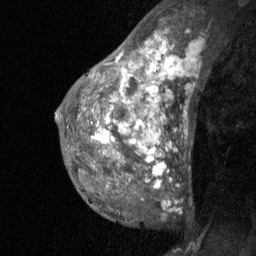
Breast MRI (dynamic contrast-enhanced), one sagittal slice. Slice 40 of 64 in the series (ordered by position). Dynamic contrast-enhanced study with each time point stored as its own series, time point 2 of 3 at this slice position (early post-contrast, ordered by acquisition time). 1.5 T. TE 4.8 ms, TR 27 ms. 2 mm slice thickness. 256 × 256 image matrix, field of view 180 × 180 mm. Patient: female, 36 years. Case-level facts recorded for this patient, not image findings: setting: breast cancer imaged before/during neoadjuvant chemotherapy; receptor status: HR-positive, HER2-negative.
Annotated regions visible in this slice (semi-automatic segmentation, software-assisted and operator-edited):
- analysis volume of interest (the breast-tissue region the enhancement analysis was run in; not a lesion): bounding box <67,12,188,226> (left, top, right, bottom; pixels)
- tumour enhancement mask (voxels above the 90 % enhancement threshold inside the analysis volume of interest): <92,36,162,187>